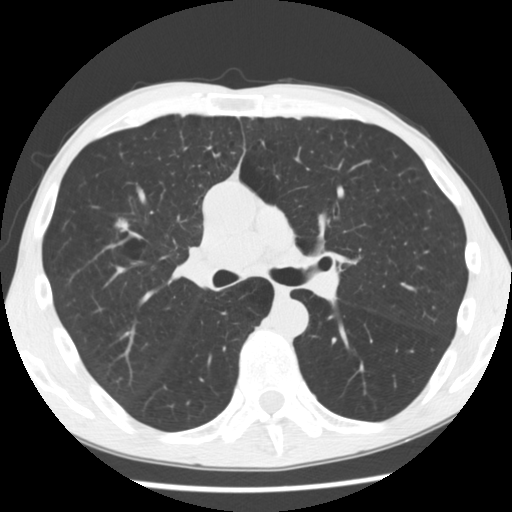
Low-dose screening chest CT, axial slice; baseline screening round; lung window (W 1500 / L -600 HU); 2.5 mm slice thickness; slice 124 of 292 in the series. Male, age 56 years at enrolment. Current smoker at enrolment.
- Expert-annotated lung lesion, bounding box [x1, y1, x2, y2] px = [99, 206, 149, 249].
- The screening reader recorded 2 non-calcified nodules or masses ≥4 mm on this exam (right upper lobe, right upper lobe); which of them this box marks is not recorded.
- Participant outcome: lung cancer diagnosed 476 days after this screen — squamous cell carcinoma, NOS, right upper lobe, right middle lobe, well differentiated (G1), stage IA (AJCC 6th edition), 27 mm at pathology.